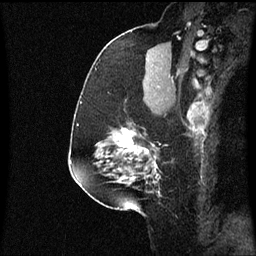
Breast MRI (dynamic contrast-enhanced), one sagittal slice. Position 39 of 60 along the scan axis. Dynamic contrast-enhanced series, image 2 of 3 at this slice position (ordered by acquisition). 1.5 T. TE 4.2 ms, TR 8.9 ms. 2 mm slice thickness. 256 × 256 image matrix, field of view 200 × 200 mm. Patient: female, 58 years. From the clinical record (not read from this slice): setting: breast cancer imaged before/during neoadjuvant chemotherapy; receptor status: triple-negative.
Annotated regions visible in this slice (semi-automatically segmented with operator editing):
- analysis volume of interest (the breast-tissue region the enhancement analysis was run in; not a lesion): bounding box [x1, y1, x2, y2] px = [104, 122, 161, 179]
- tumour enhancement mask (voxels above the 70 % enhancement threshold inside the analysis volume of interest): [116, 128, 157, 179]